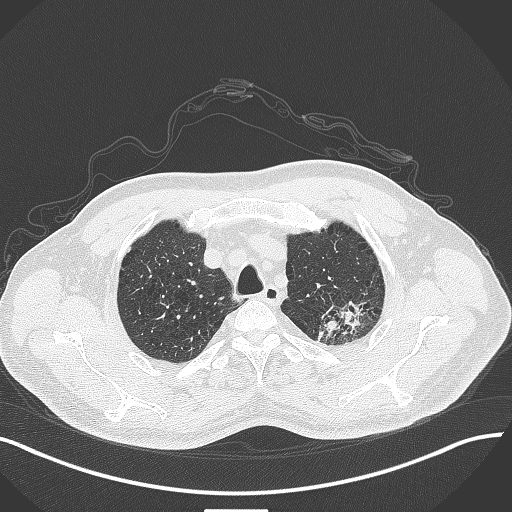
Chest CT, one axial slice; position 355 of 429 along the scan axis; reconstruction kernel B70f; 120 kVp; lung window (W 1500 / L -600 HU); 1 mm slice thickness; 512 × 512 image matrix, field of view 400 × 400 mm. Male patient, age 55 years. From the clinical record (not read from this slice): clinical TNM (as recorded): T3 N0 M1c.
Outlined on this slice (rectangle marked by the reading radiologist):
- lung tumour (recorded histology: adenocarcinoma): bounding box [x1, y1, x2, y2] px = [316, 296, 384, 349]